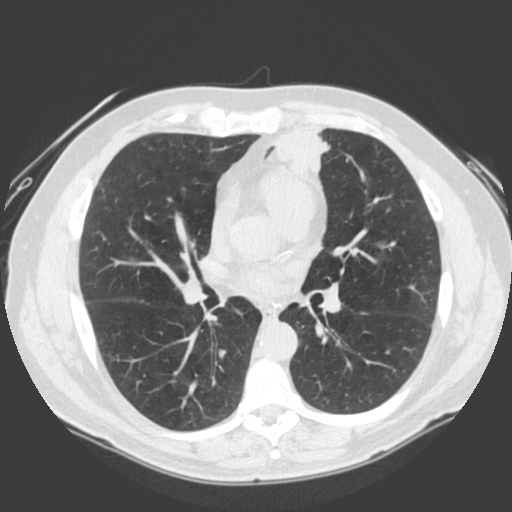
Low-dose screening chest CT, one axial slice. Position 98 of 185 along the scan axis. 120 kVp. Lung window (W 1500 / L -600 HU). 2 mm slice thickness. 512 × 512 image matrix, field of view 360 × 360 mm.
Structures marked on this image (expert manual segmentation):
- lesion 1 (tumor, lower lobe of left lung): bounding box <275,128,331,174> (left, top, right, bottom; pixels)